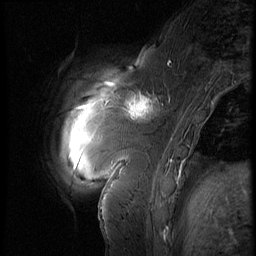
Breast MRI (dynamic contrast-enhanced), one sagittal slice. Position 14 of 60 along the scan axis. 3 images stored at this slice position (order not interpretable as contrast timing). 1.5 T. TE 4.2 ms, TR 9 ms. 256 × 256 image matrix, field of view 180 × 180 mm. Female patient, age 57 years. Case-level facts recorded for this patient, not image findings: setting: breast cancer imaged before/during neoadjuvant chemotherapy; receptor status: triple-negative.
Outlined on this slice (semi-automatic segmentation, software-assisted and operator-edited):
- analysis volume of interest (the breast-tissue region the enhancement analysis was run in; not a lesion): bounding box <114,83,170,131> (left, top, right, bottom; pixels)
- tumour enhancement mask (voxels above the 140 % enhancement threshold inside the analysis volume of interest): <114,85,153,118>